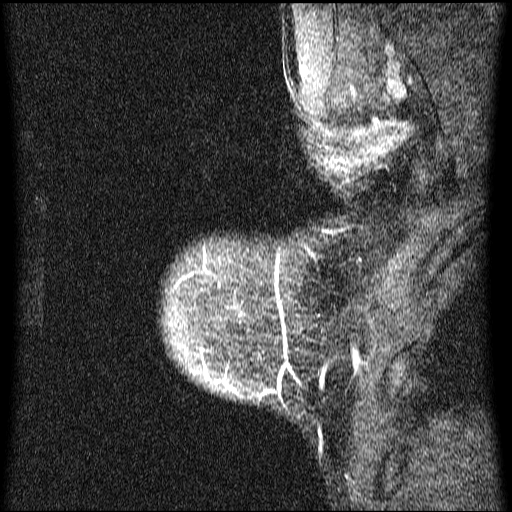
Breast MRI (dynamic contrast-enhanced), one sagittal slice; position 57 of 64 along the scan axis; dynamic contrast-enhanced series, image 2 of 4 at this slice position (ordered by acquisition); 1.5 T; TE 4.2 ms, TR 9.1 ms; 2 mm slice thickness; 512 × 512 image matrix, field of view 180 × 180 mm. Patient: female, 33 years.
Annotated regions visible in this slice (semi-automatic segmentation, software-assisted and operator-edited):
- analysis volume of interest (the breast-tissue region the enhancement analysis was run in; not a lesion): bounding box (x1, y1, x2, y2) in pixels: (167, 162, 335, 432)
- tumour enhancement mask (voxels above the 70 % enhancement threshold inside the analysis volume of interest): (201, 315, 281, 396)